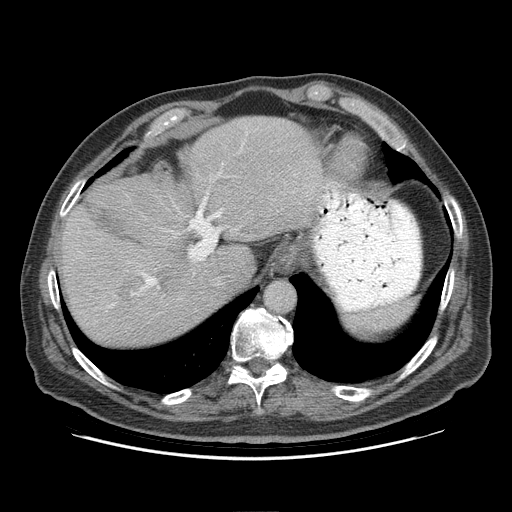
Contrast-enhanced abdominal CT (liver protocol), one axial slice. Position 71 of 95 along the scan axis. Reconstruction kernel STANDARD. 140 kVp. Soft-tissue window (W 400 / L 40 HU). 2.5 mm slice thickness. 512 × 512 image matrix. From the clinical record (not read from this slice): diagnosis: hepatocellular carcinoma (patient treated with transarterial chemoembolisation; whether this scan precedes or follows treatment is not stated here); TNM stage (as recorded): Stage-IVB; Child-Pugh class: A.
Outlined on this slice (semi-automatic segmentation, software-assisted and operator-edited):
- abdominal aorta: bounding box (x1, y1, x2, y2) in pixels: (266, 282, 293, 313)
- liver parenchyma outside the tumour (the mass and vessels are separate outlines, so this box may not span the whole liver): (60, 116, 324, 344)
- mass: (115, 271, 142, 301)
- liver vessels: (141, 197, 221, 290)